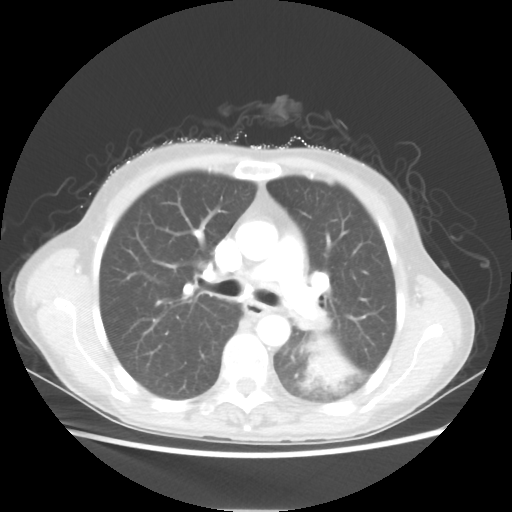
Chest CT, one axial slice. Slice 35 of 56 in the series (ordered by position). Reconstruction kernel STANDARD. Lung window (W 1500 / L -600 HU). 512 × 512 image matrix, field of view 360 × 360 mm. Patient: female, 53 years. From the clinical record (not read from this slice): clinical TNM (as recorded): T3 N0 M0.
Outlined on this slice (bounding box drawn by a radiologist):
- lung tumour (recorded histology: adenocarcinoma): box from (x=301, y=331) to (x=355, y=390) px